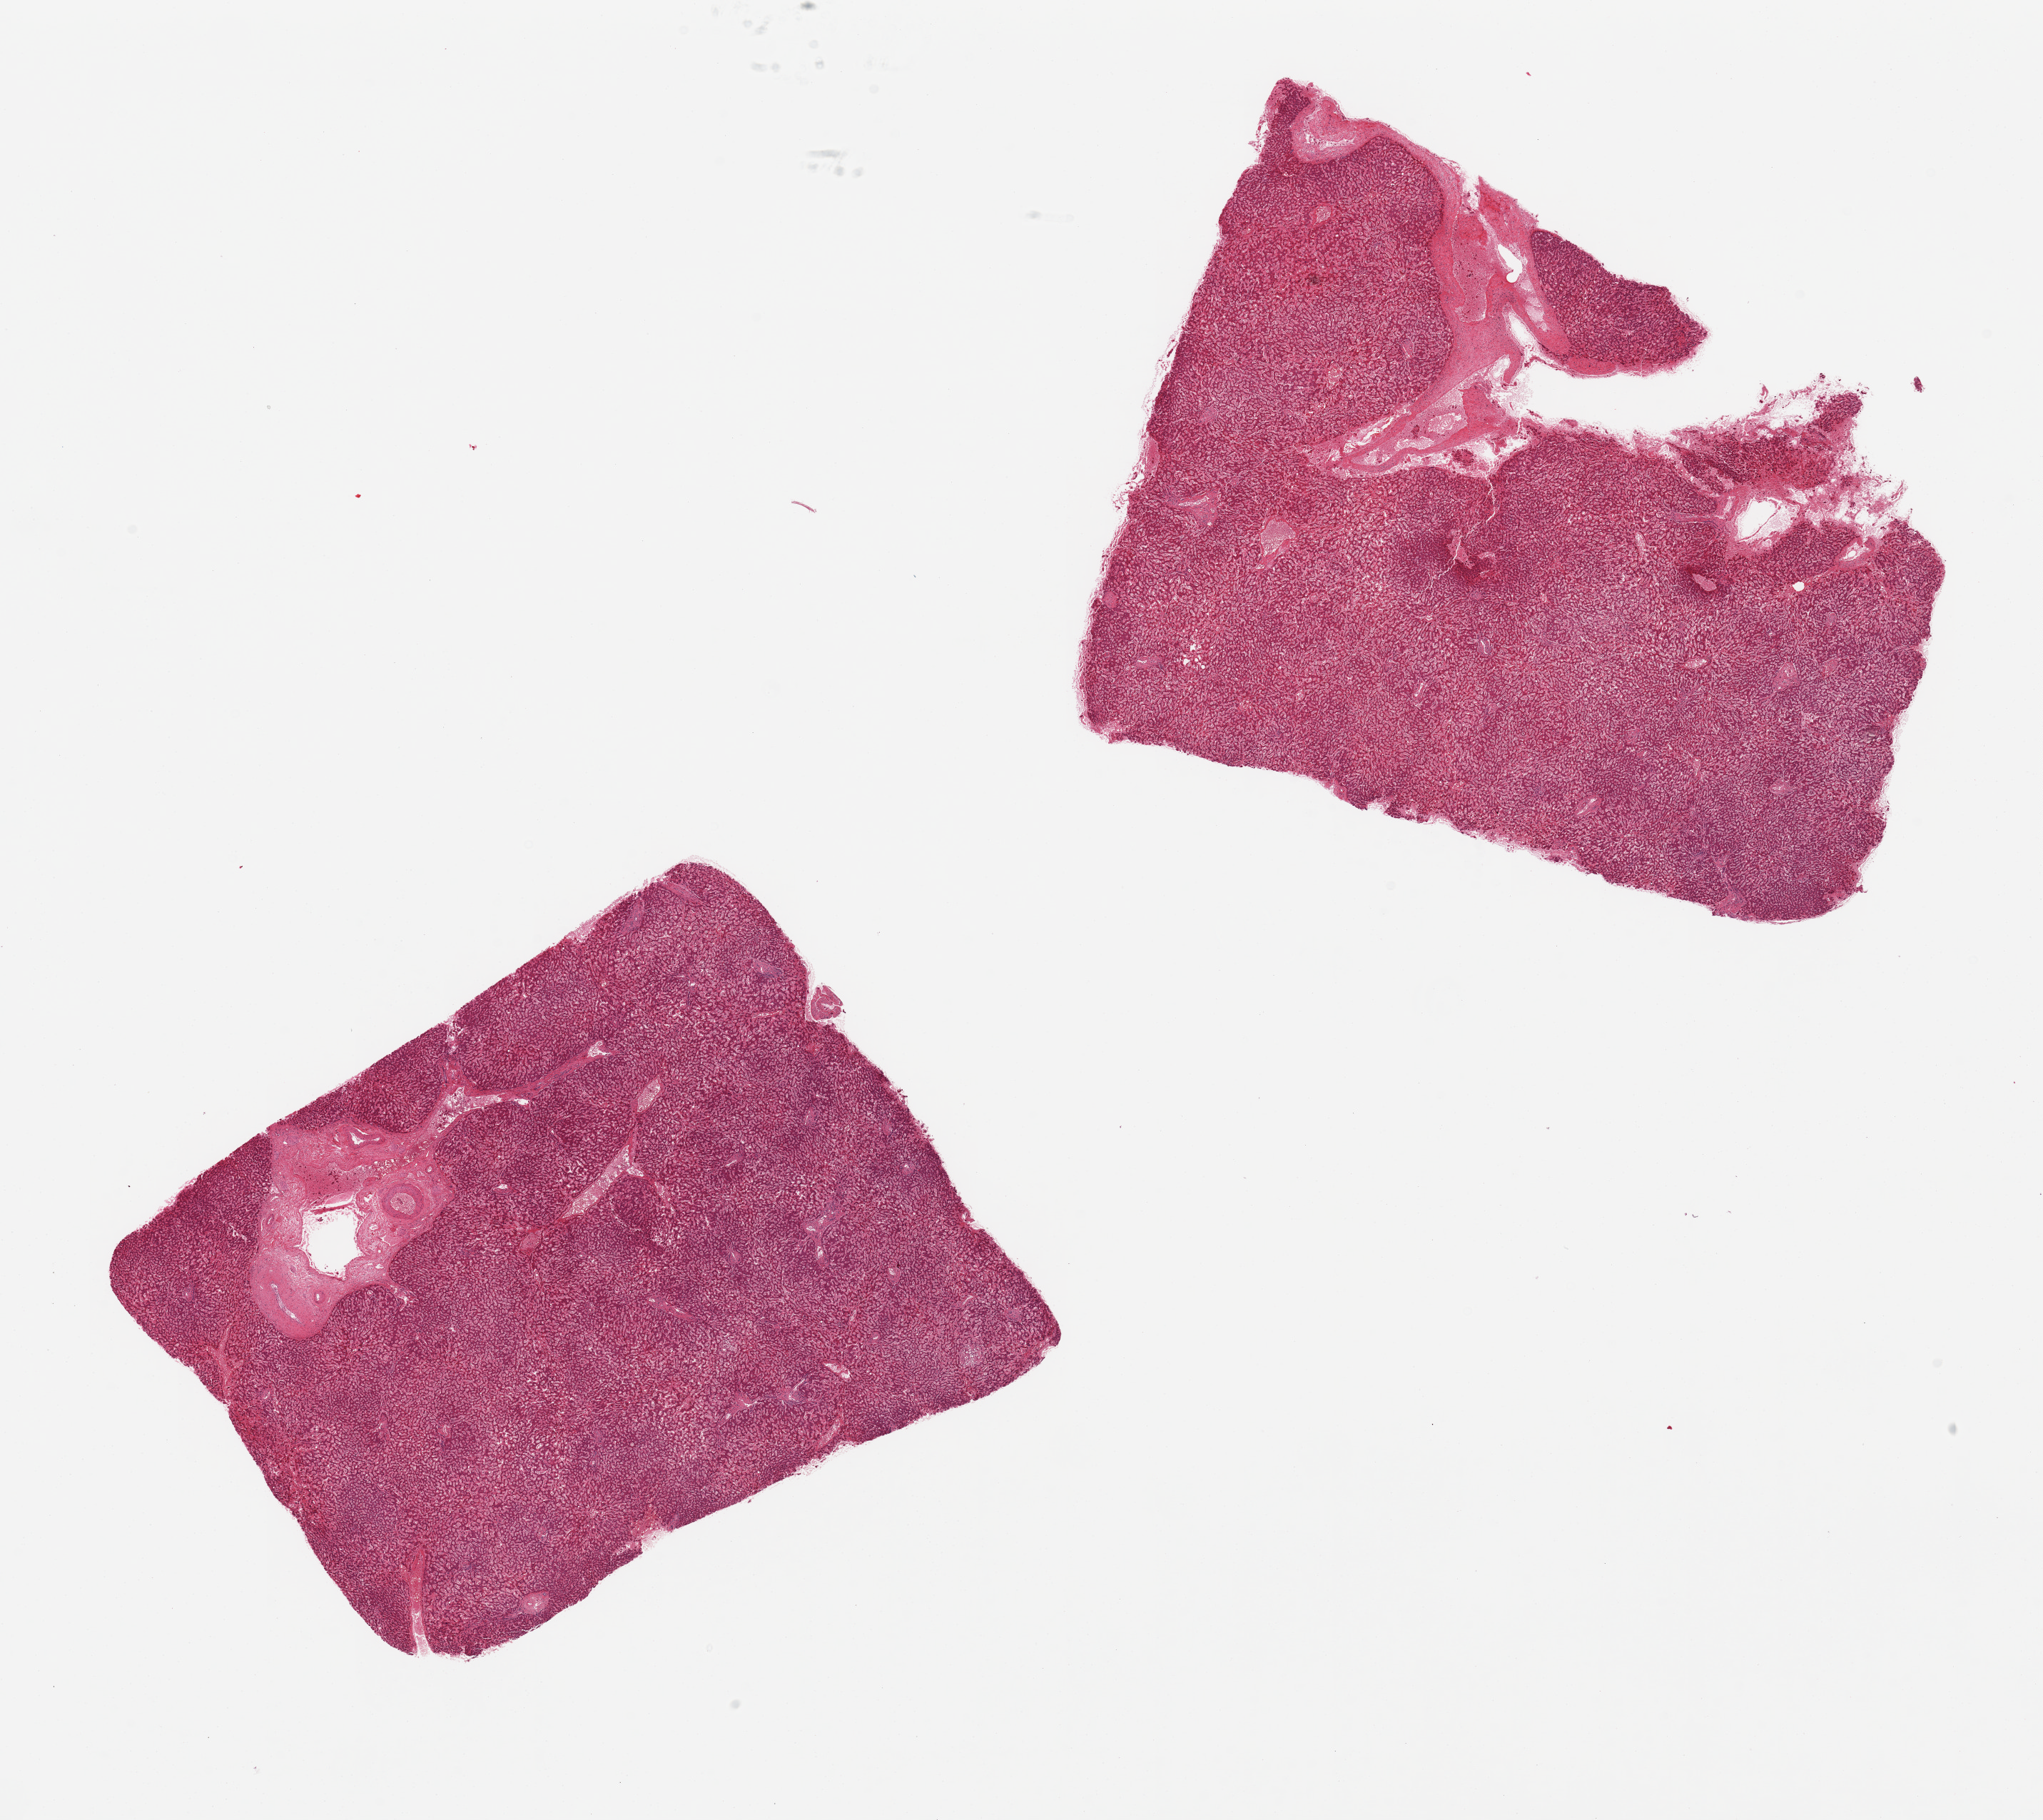
Digitized haematoxylin and eosin-stained section, low-resolution overview of the scanned area, about 22.6 x 20.2 mm (acquisition: 20x scan). PAXgene-fixed paraffin-embedded (PFPE) section. Sampled site (target tissue): liver. Donor tissue sample. Male donor.
Review note (as recorded): 2 pieces, moderate congestion; minimal steatosis.